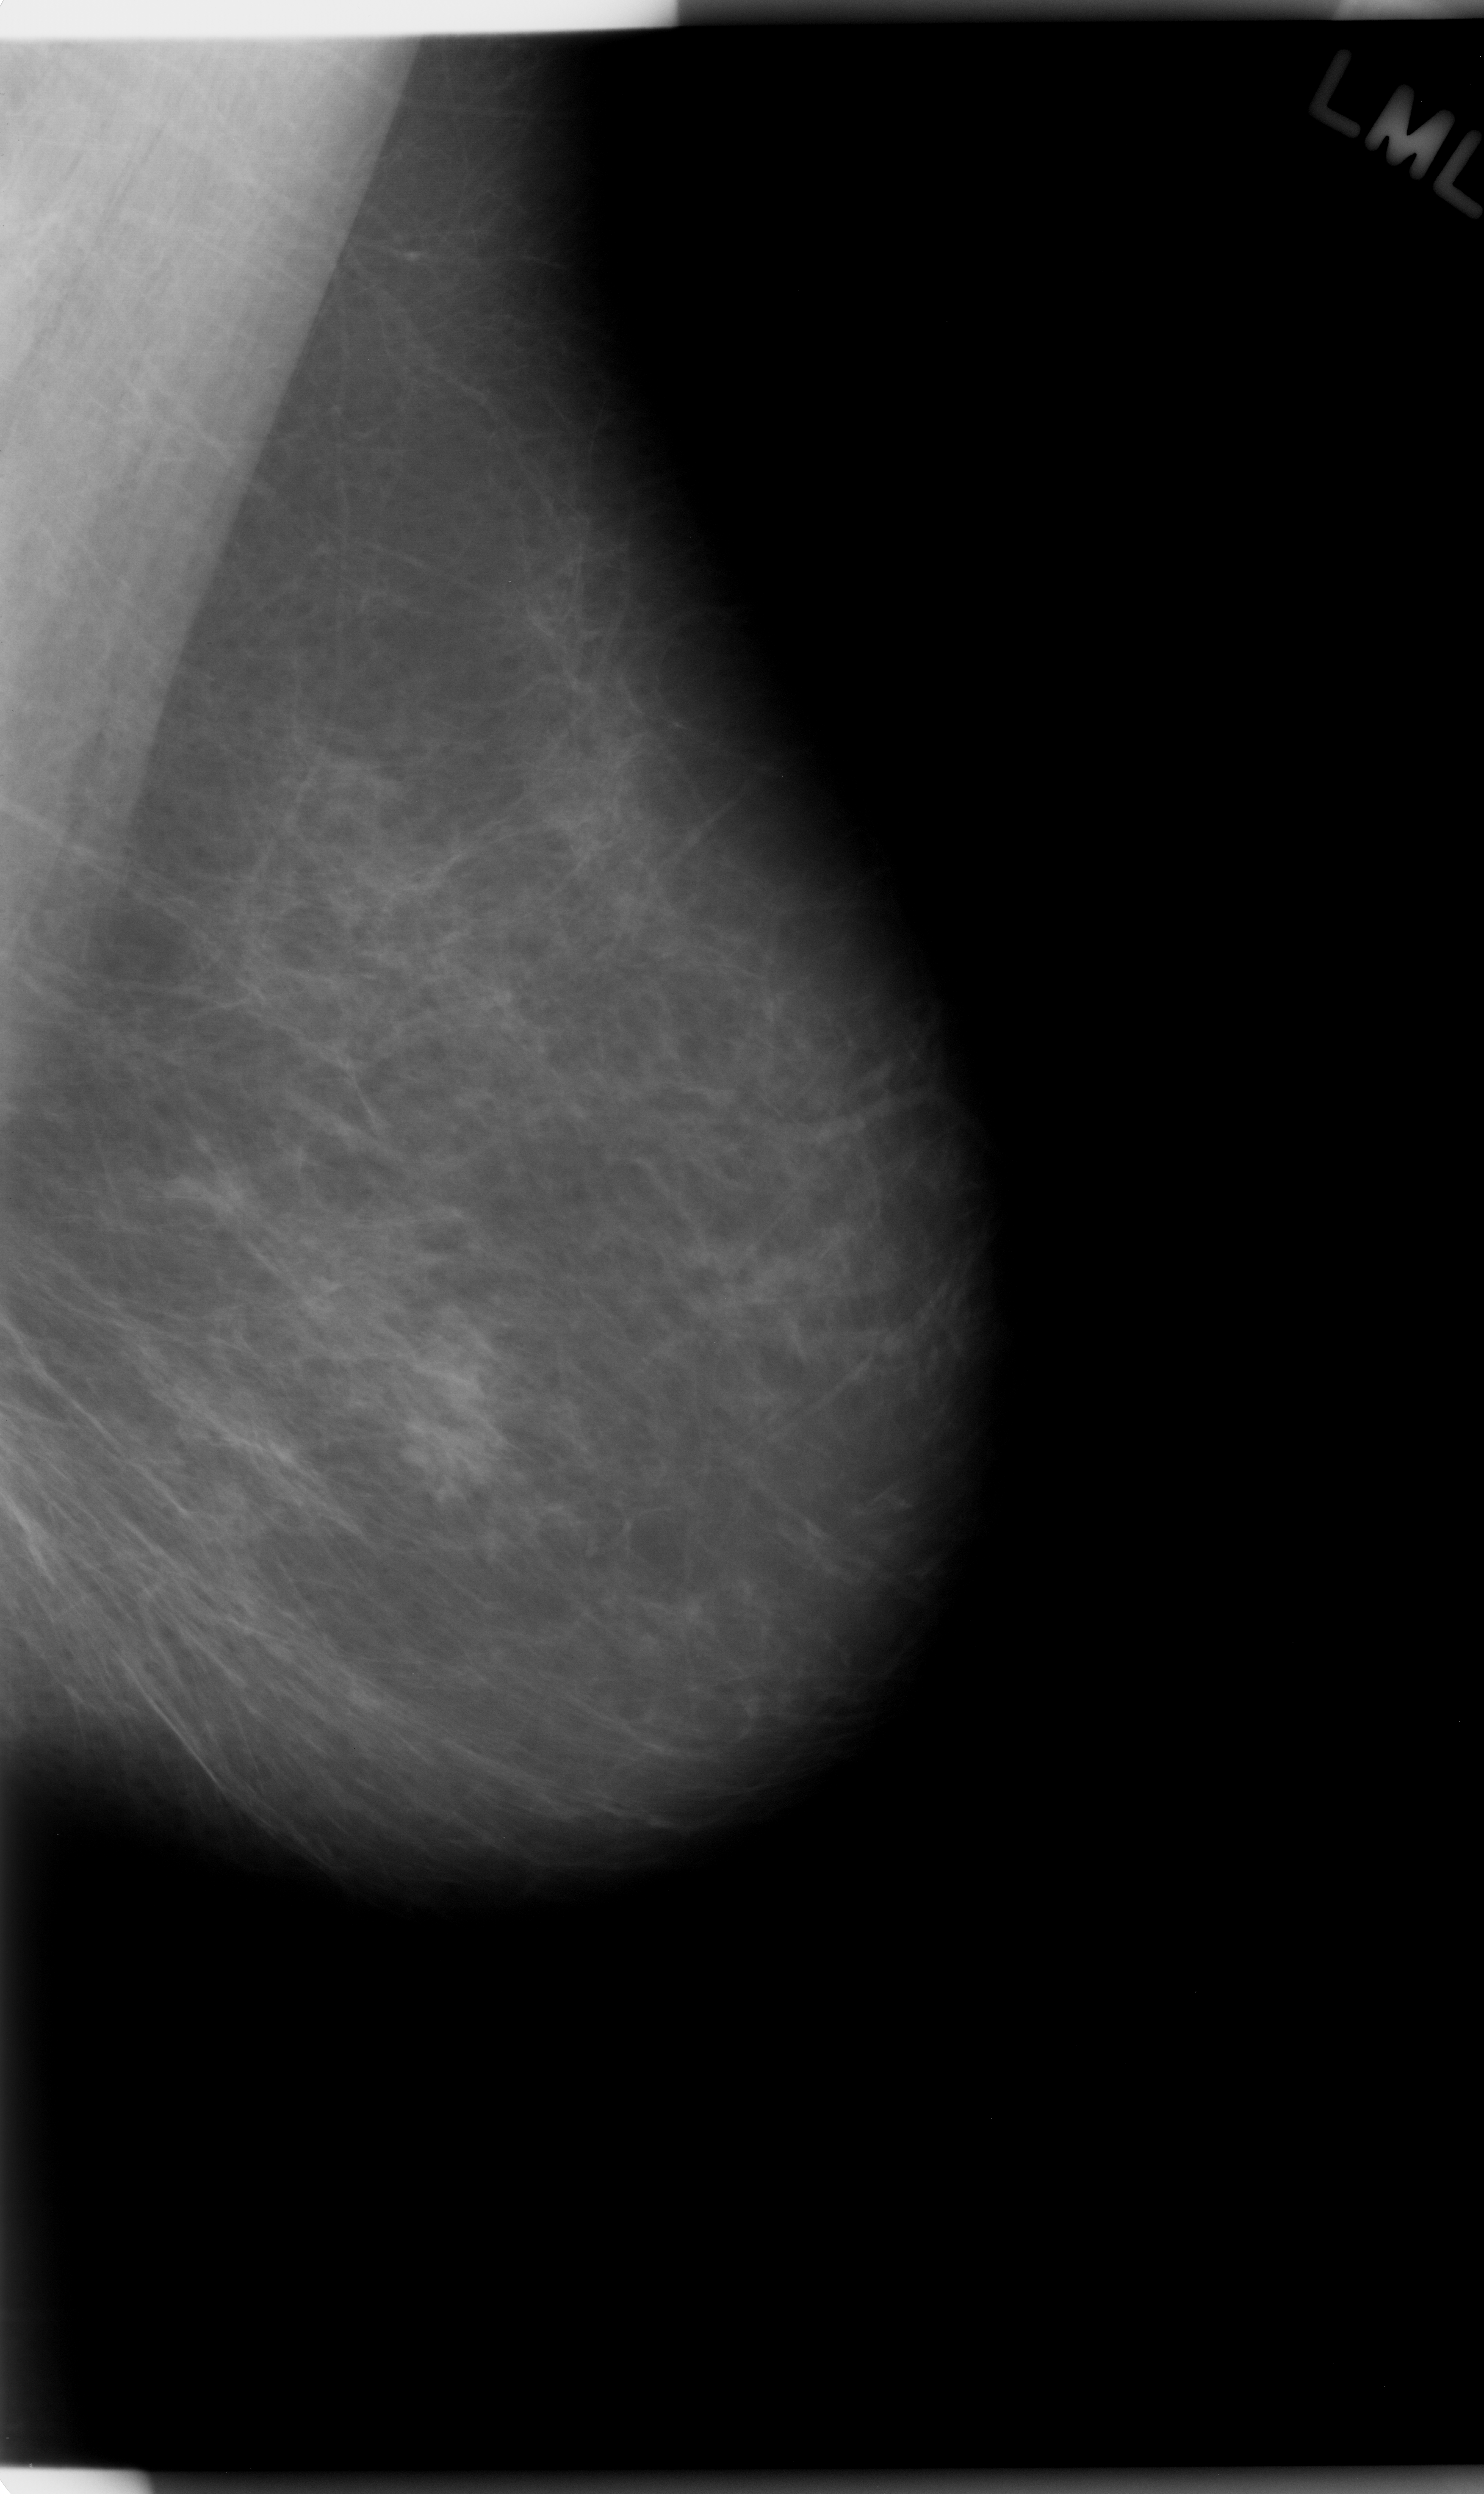
Scanned film-screen mammogram; left breast; mediolateral oblique (MLO) view; BI-RADS breast density category 1 (scale 1–4).
Abnormality record for this image: mass, shape lobulated, margins ill defined; BI-RADS assessment category 4; subtlety rating 4 on a 1 (subtle) to 5 (obvious) scale; pathology (as recorded): malignant.